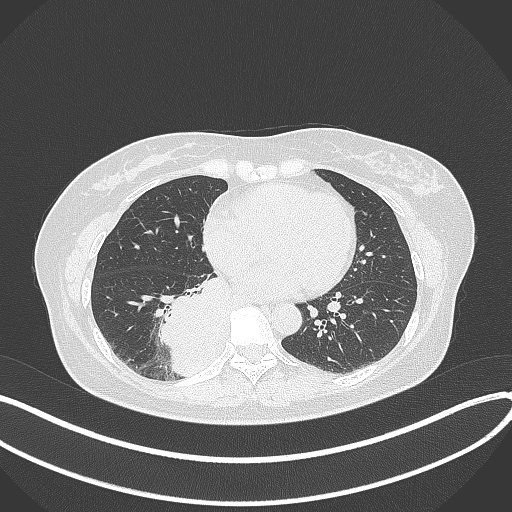
Chest CT, one axial slice. Position 140 of 331 along the scan axis. 120 kVp. Lung window (W 1500 / L -600 HU). 1 mm slice thickness. 512 × 512 image matrix, field of view 400 × 400 mm. Female patient, age 54 years. Case-level facts recorded for this patient, not image findings: clinical TNM (as recorded): T4 N0 M0.
Structures marked on this image (rectangle marked by the reading radiologist):
- lung tumour (recorded histology: adenocarcinoma): bounding box (x1, y1, x2, y2) in pixels: (158, 271, 232, 381)